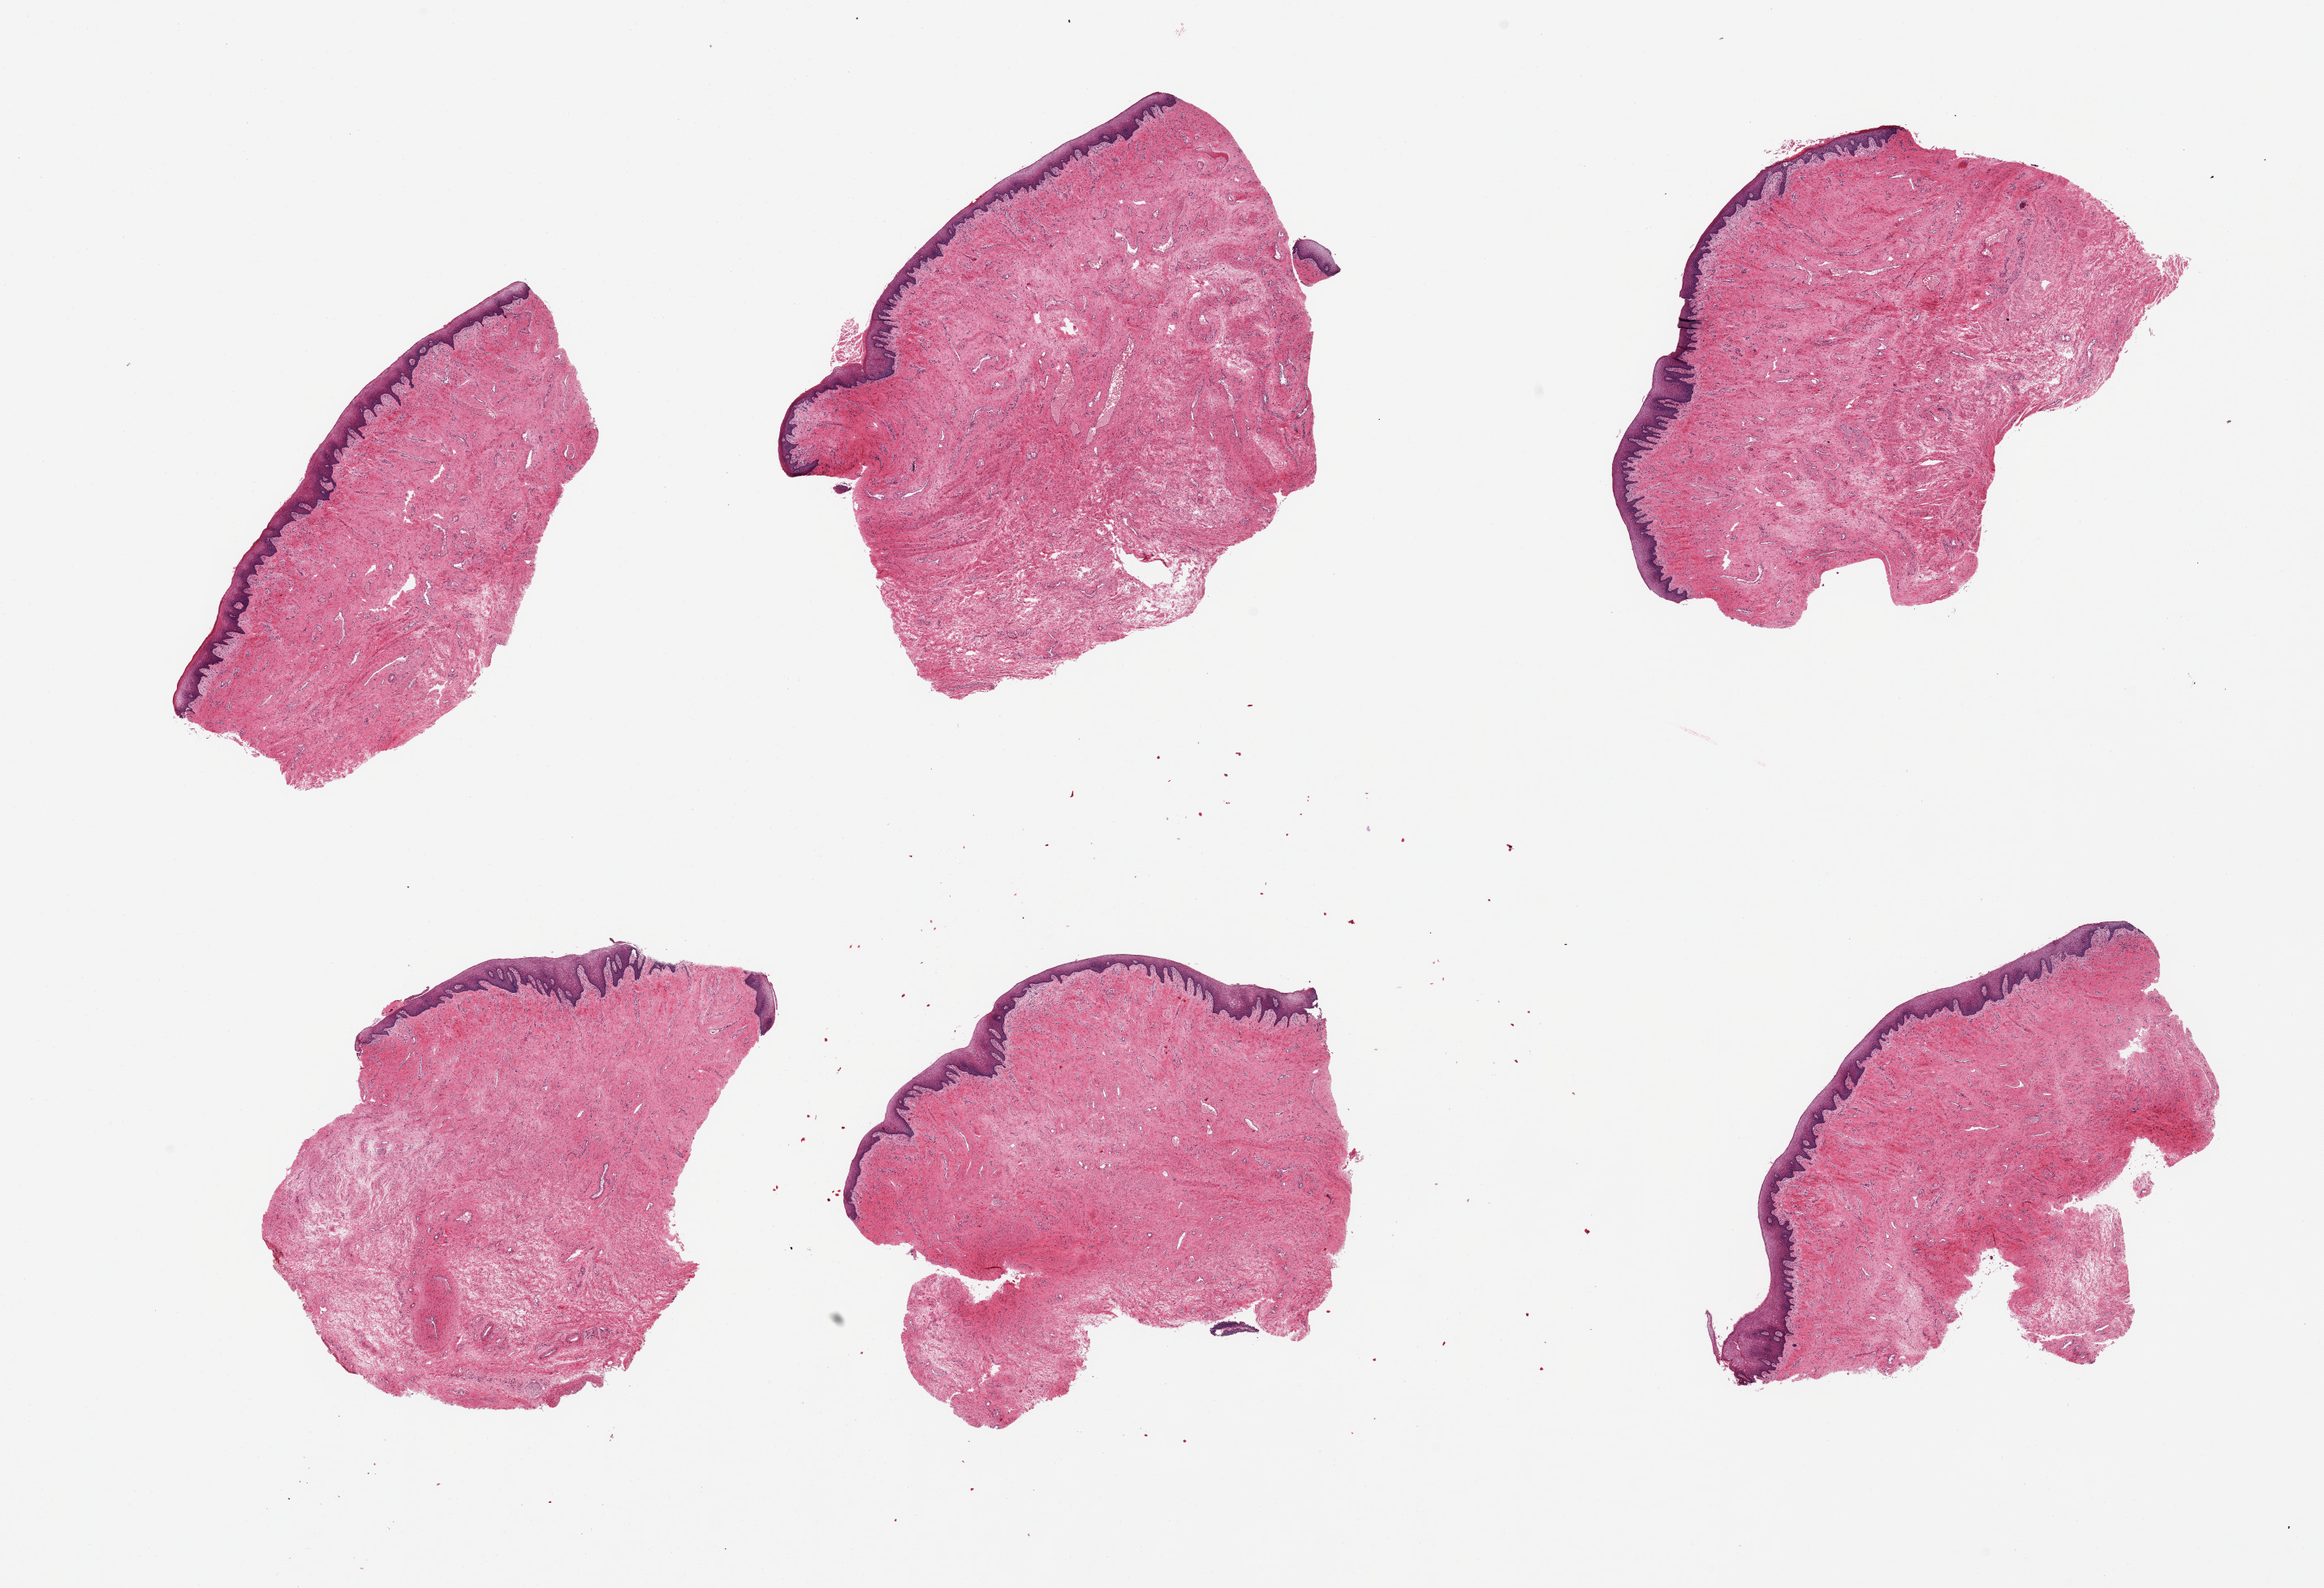
Whole-slide image, H&E stain — whole scanned area (about 22.6 x 15.5 mm, slide scanned at 20x) shown as a low-resolution overview. PAXgene-fixed paraffin-embedded (PFPE) section. Target tissue: vagina. Tissue donor sample. Donor sex: female.
Reviewer comment on this tissue sample: 6 pieces, squamous mucosa up to ~0.2mm.